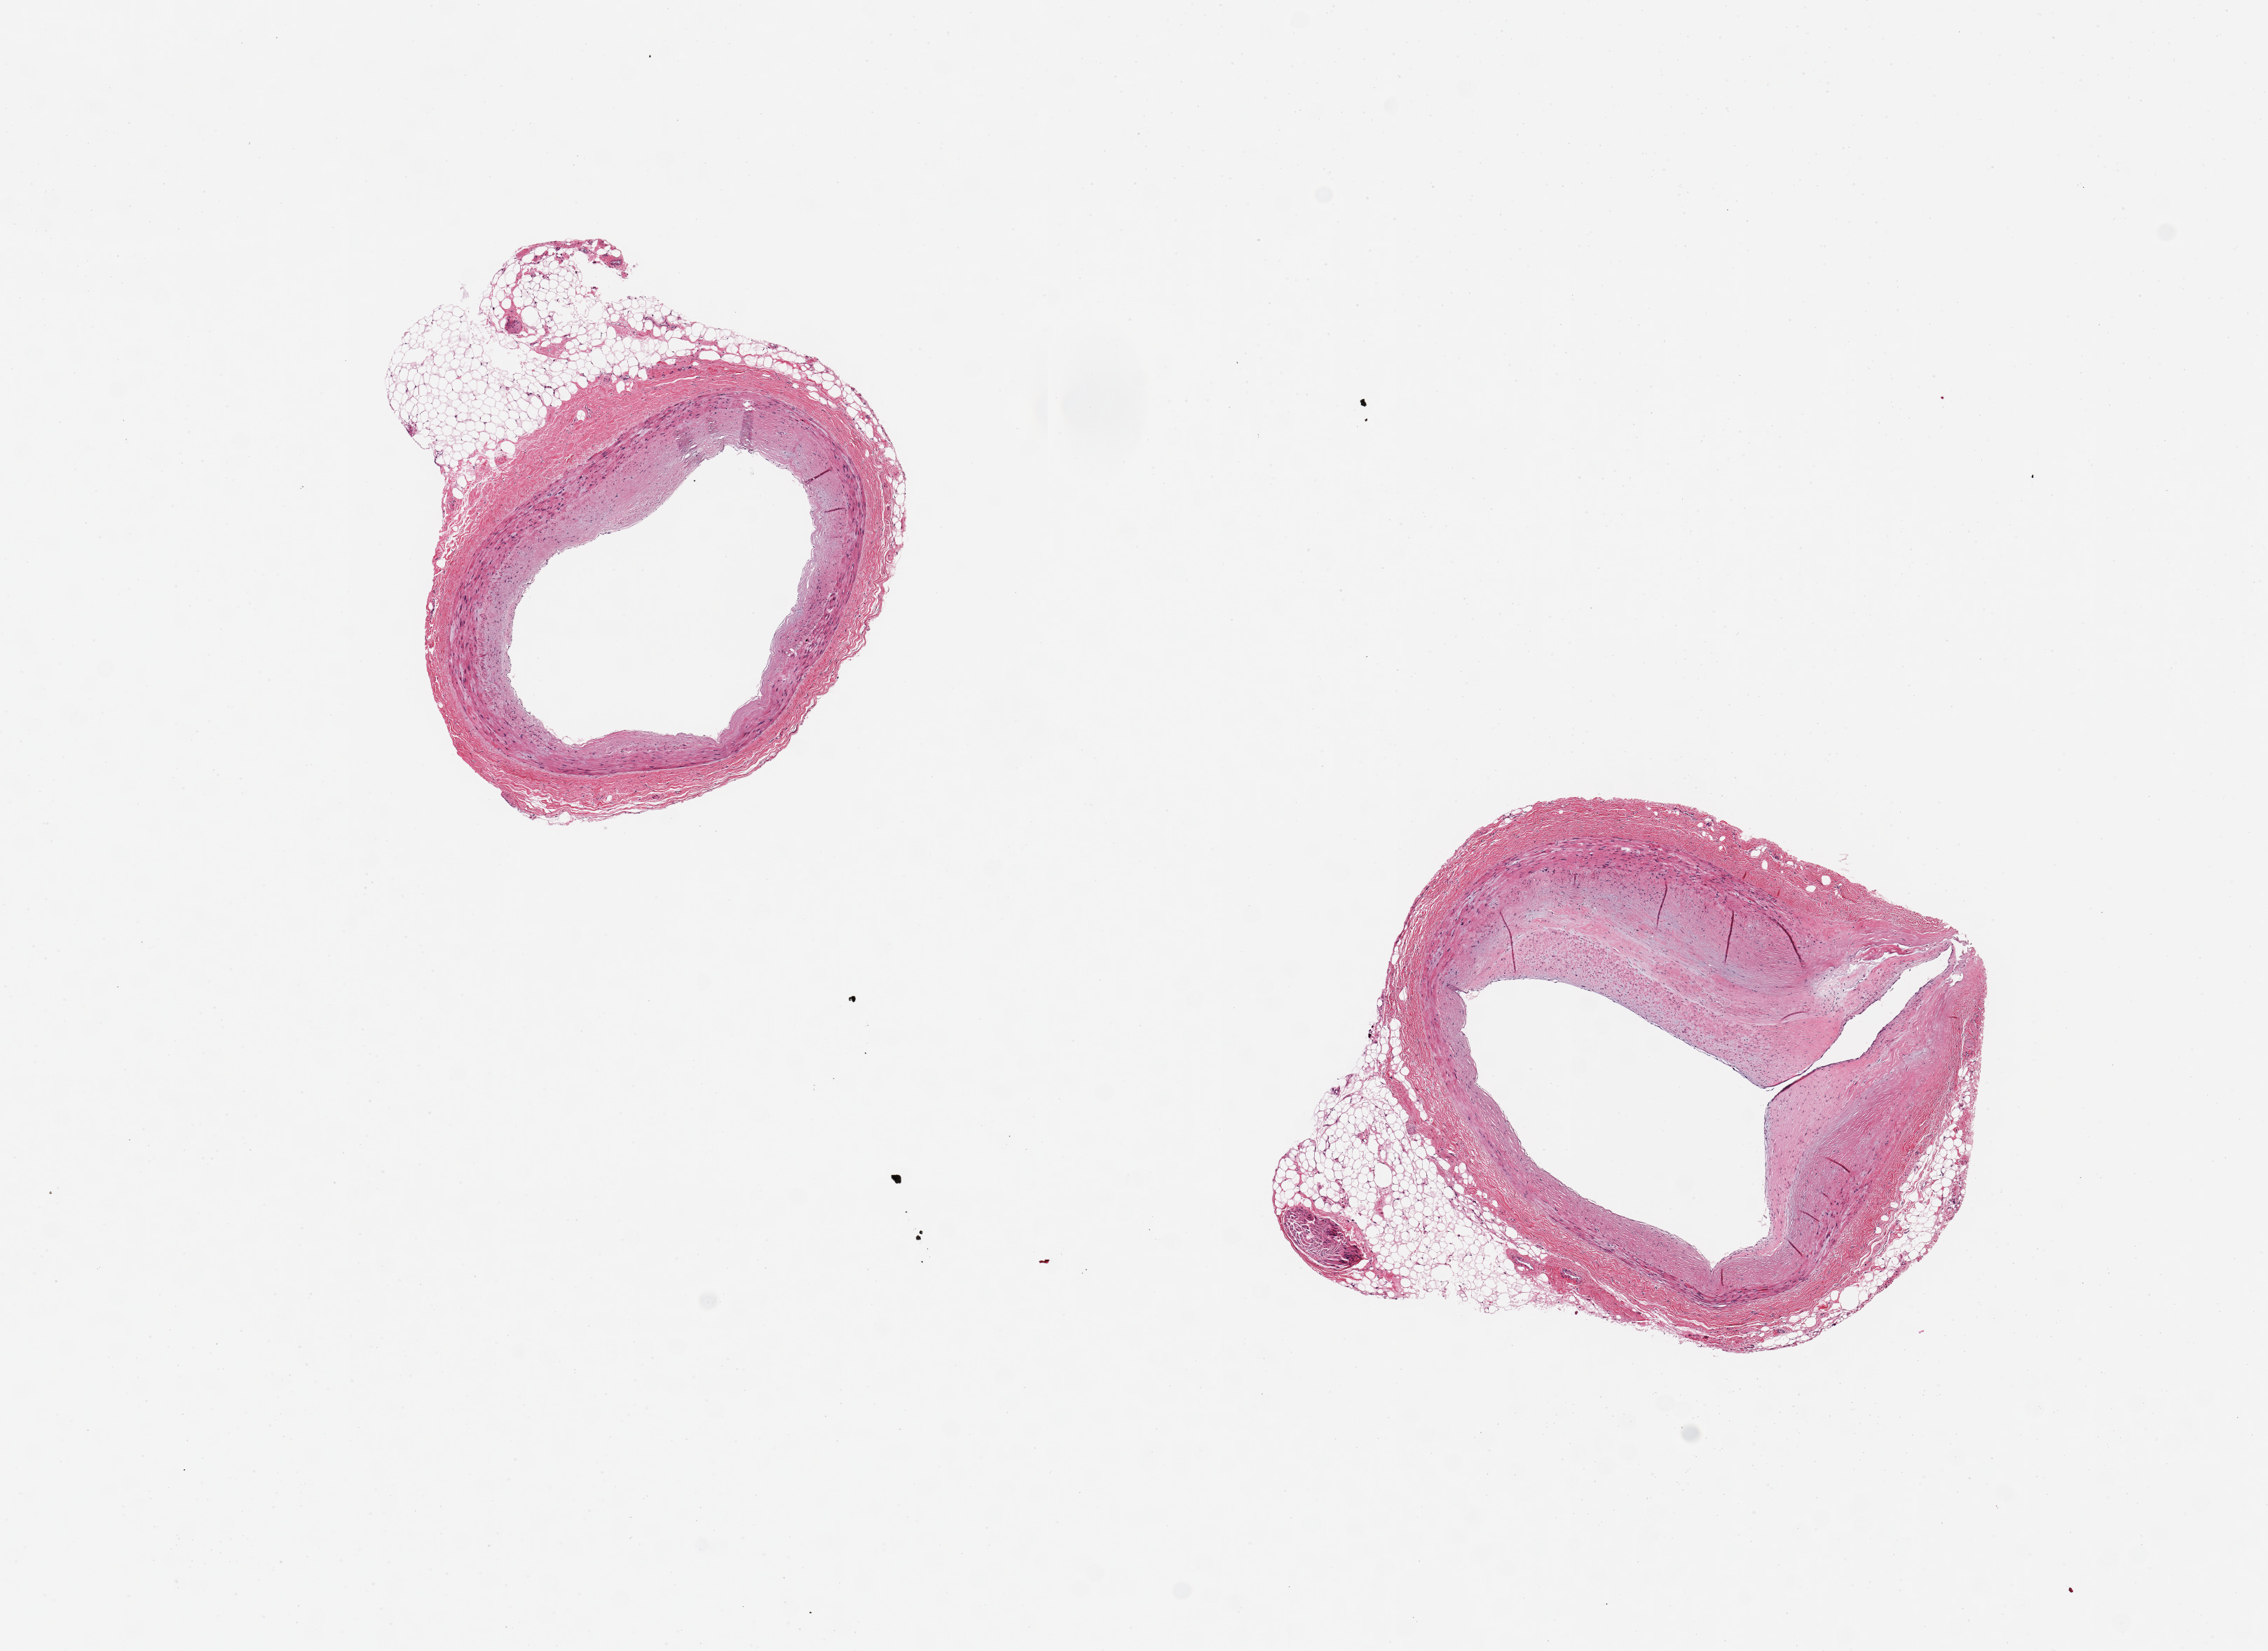
Whole-slide image, haematoxylin and eosin stain, low-resolution overview of the scanned area, about 12.8 x 9.3 mm; PAXgene-fixed, paraffin-embedded tissue; sampled site (target tissue): coronary artery; donor tissue sample. Donor: female.
Pathologist's review note for this sample: 2 aliquots, ~3mm d, mild atherosclerosis (<20% occlusion), one aliquot with nubbin of fat.